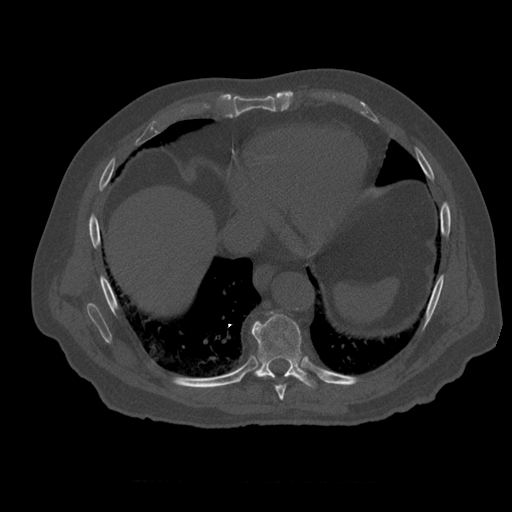
CT including the spine, one axial slice. Slice 327 of 399 in the series (ordered by position). 120 kVp. Bone window (W 1800 / L 400 HU). 1.25 mm slice thickness. 512 × 512 image matrix, field of view 407 × 407 mm. Patient age 73 years. From the clinical record (not read from this slice): primary cancer: prostate; vertebrae with lytic lesions (as recorded): L2.
Outlined on this slice (semi-automatic segmentation, software-assisted and operator-edited):
- T8 vertebra: box from (x=264, y=375) to (x=289, y=401) px
- T9 vertebra: (x=251, y=312)–(x=317, y=389)